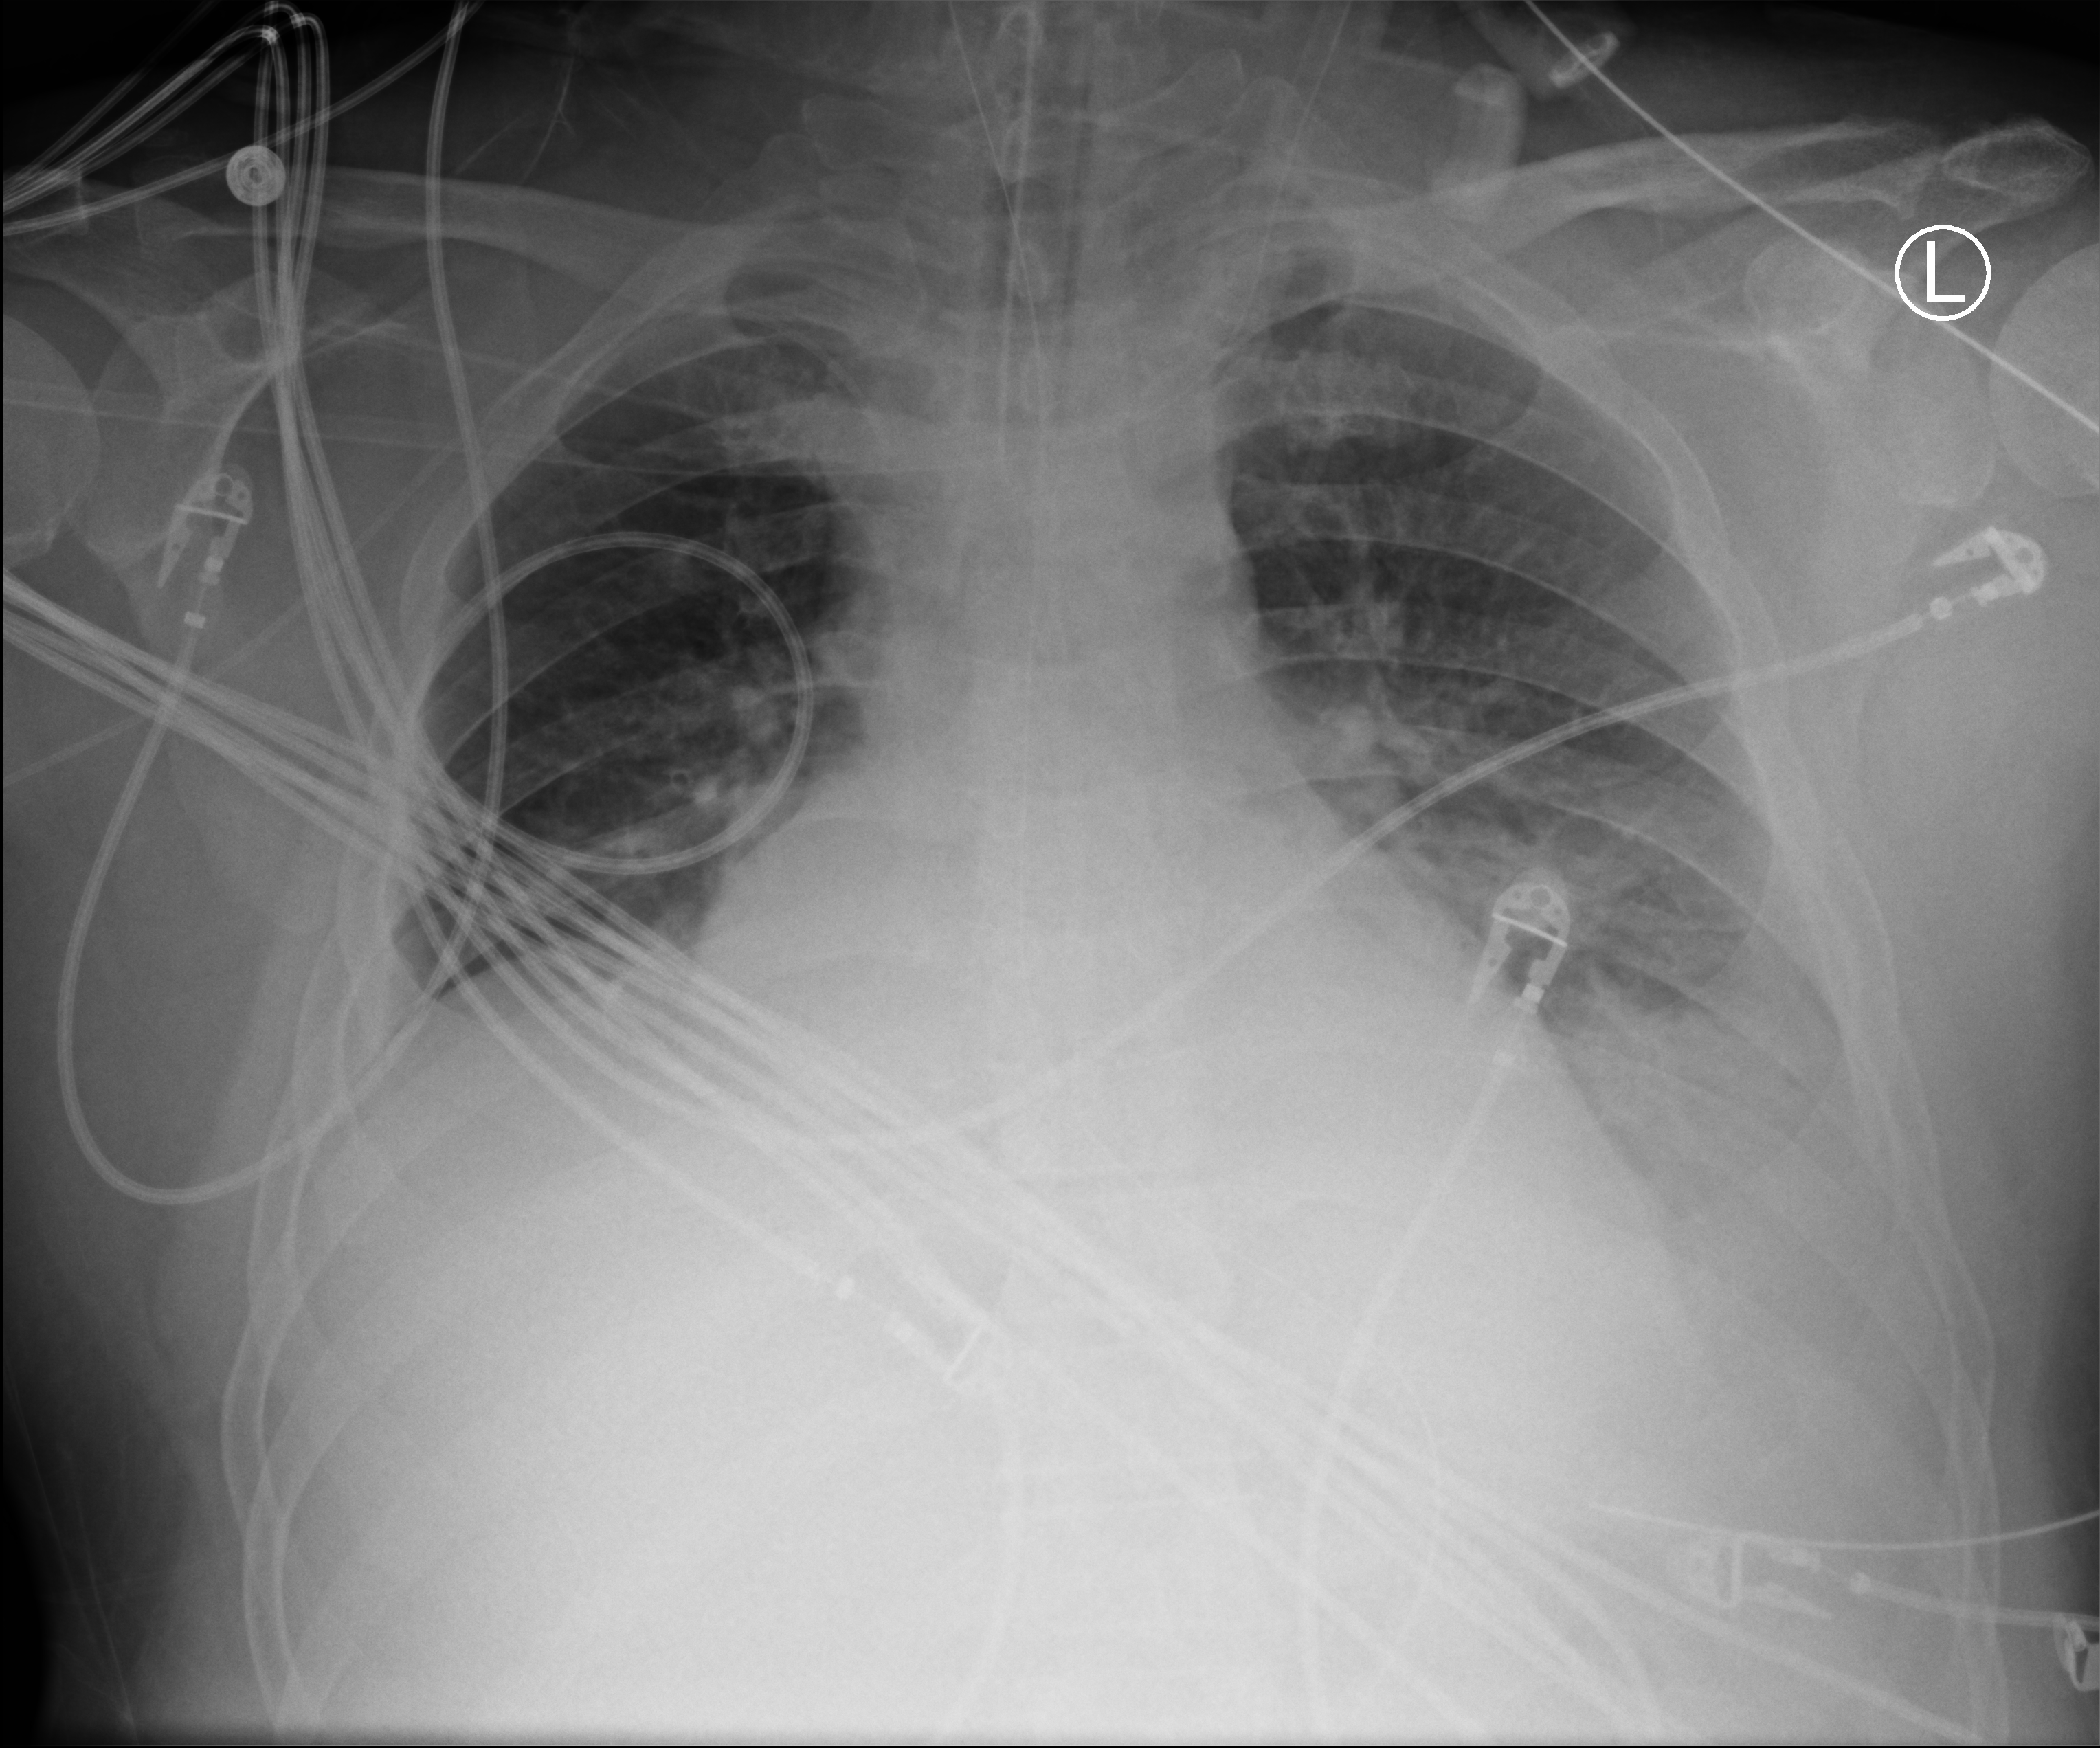
Bedside chest radiograph (computed radiography); anteroposterior (AP) projection. Male patient hospitalised with COVID-19, age 18–59 years.
Hospital-stay facts (about this admission, not read from this image; timing relative to this image not recorded):
- mechanically ventilated during this hospital stay: yes